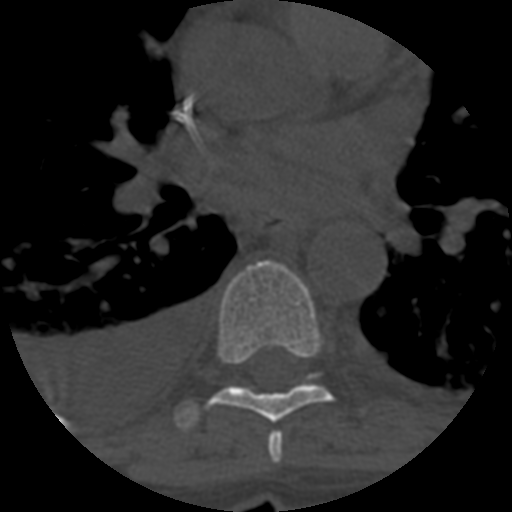
CT including the spine, one axial slice; position 415 of 708 along the scan axis; reconstruction kernel STANDARD; 120 kVp; one of 3 acquisitions stored at this slice position; bone window (W 1800 / L 400 HU); 1.25 mm slice thickness; 512 × 512 image matrix, field of view 160 × 160 mm. Patient age 55 years. From the clinical record (not read from this slice): primary cancer: colon.
Outlined on this slice (semi-automatic segmentation, software-assisted and operator-edited):
- T6 vertebra: bounding box [x1, y1, x2, y2] px = [267, 432, 283, 463]
- T7 vertebra: [176, 260, 332, 428]
- T8 vertebra: [309, 373, 320, 379]